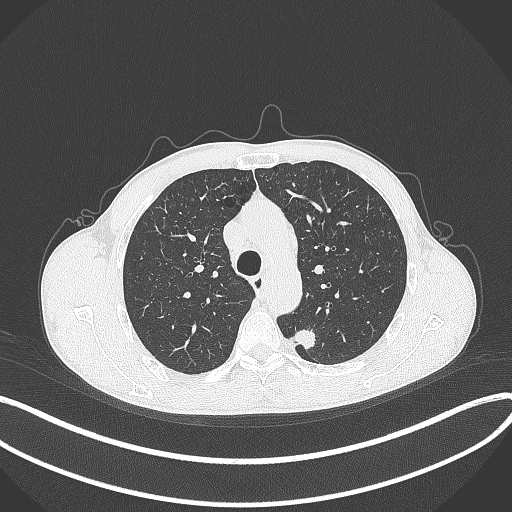
Chest CT, one axial slice. Slice 285 of 429 in the series (ordered by position). Reconstruction kernel B70f. Lung window (W 1500 / L -600 HU). 1 mm slice thickness. 512 × 512 image matrix, field of view 400 × 400 mm. Patient: male, 51 years. Case-level facts recorded for this patient, not image findings: clinical TNM (as recorded): T2a N1 M1.
Annotated regions visible in this slice (bounding box drawn by a radiologist):
- lung tumour (recorded histology: adenocarcinoma): bounding box <290,325,320,355> (left, top, right, bottom; pixels)